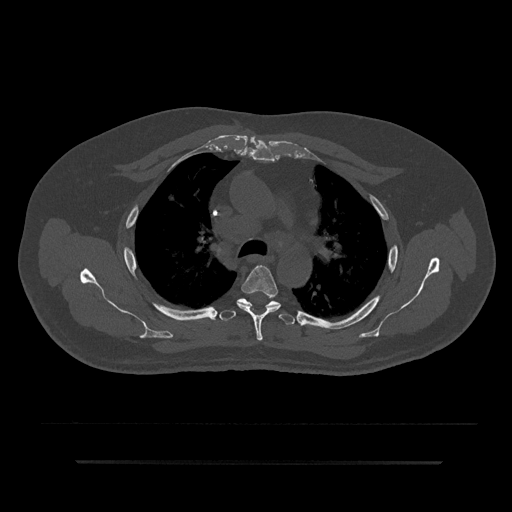
CT including the spine, one axial slice. Slice 604 of 797 in the series (ordered by position). Reconstruction kernel Br40s/3. 120 kVp. Bone window (W 1800 / L 400 HU). 0.5 mm slice thickness. 512 × 512 image matrix, field of view 464 × 464 mm. Male patient, age 59 years. From the clinical record (not read from this slice): primary cancer: bile ducts.
Annotated regions visible in this slice (semi-automatically segmented with operator editing):
- T4 vertebra: bounding box (x1, y1, x2, y2) in pixels: (237, 265, 281, 341)
- T5 vertebra: (220, 298, 297, 325)